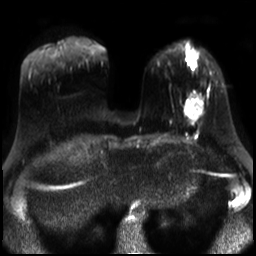
Breast MRI, one axial slice; position 8 of 30 along the scan axis; diffusion-weighted series; image 2 of 4 stored at this slice position (different b-values; order by instance number); 3 T; 4 mm slice thickness; 256 × 256 image matrix, field of view 320 × 320 mm. Female patient.
Annotated regions visible in this slice (manually delineated by an expert):
- tumour on diffusion-weighted imaging: bounding box <185,104,201,120> (left, top, right, bottom; pixels)